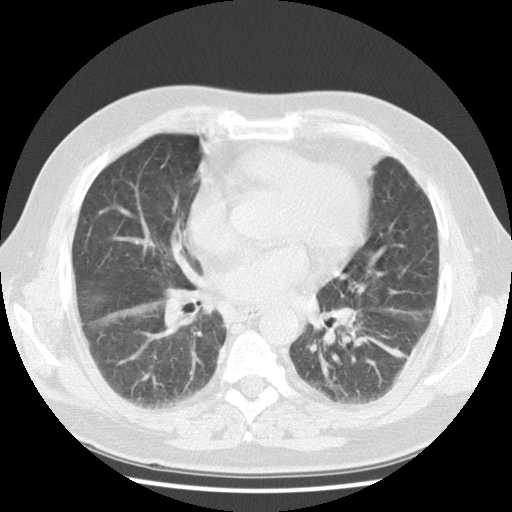
Low-dose screening chest CT, one axial slice; position 56 of 108 along the scan axis; 120 kVp; lung window (W 1500 / L -600 HU); 2.5 mm slice thickness; 512 × 512 image matrix, field of view 350 × 350 mm.
Annotated regions visible in this slice (outlined manually by an expert reader):
- lesion 1 (tumor, hilum of left lung): bounding box [x1, y1, x2, y2] px = [336, 305, 358, 329]